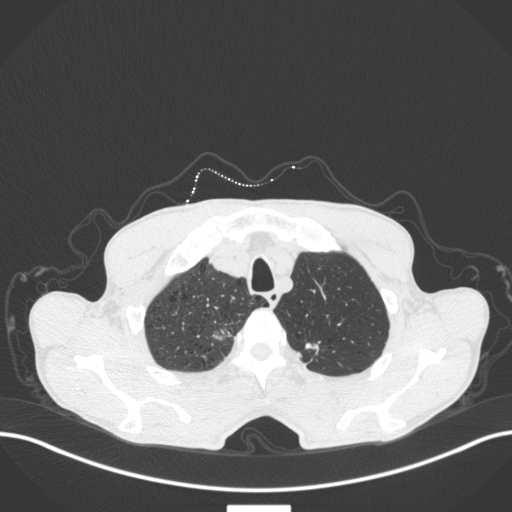
Chest CT, one axial slice. Slice 375 of 445 in the series (ordered by position). Reconstruction kernel B31f. Lung window (W 1500 / L -600 HU). 1 mm slice thickness. 512 × 512 image matrix, field of view 400 × 400 mm. Patient: male, 70 years. From the clinical record (not read from this slice): clinical TNM (as recorded): T1a N0 M0; histopathological grade: G1-2.
Structures marked on this image (bounding box drawn by a radiologist):
- lung tumour (recorded histology: adenocarcinoma): bounding box [x1, y1, x2, y2] px = [210, 321, 233, 342]